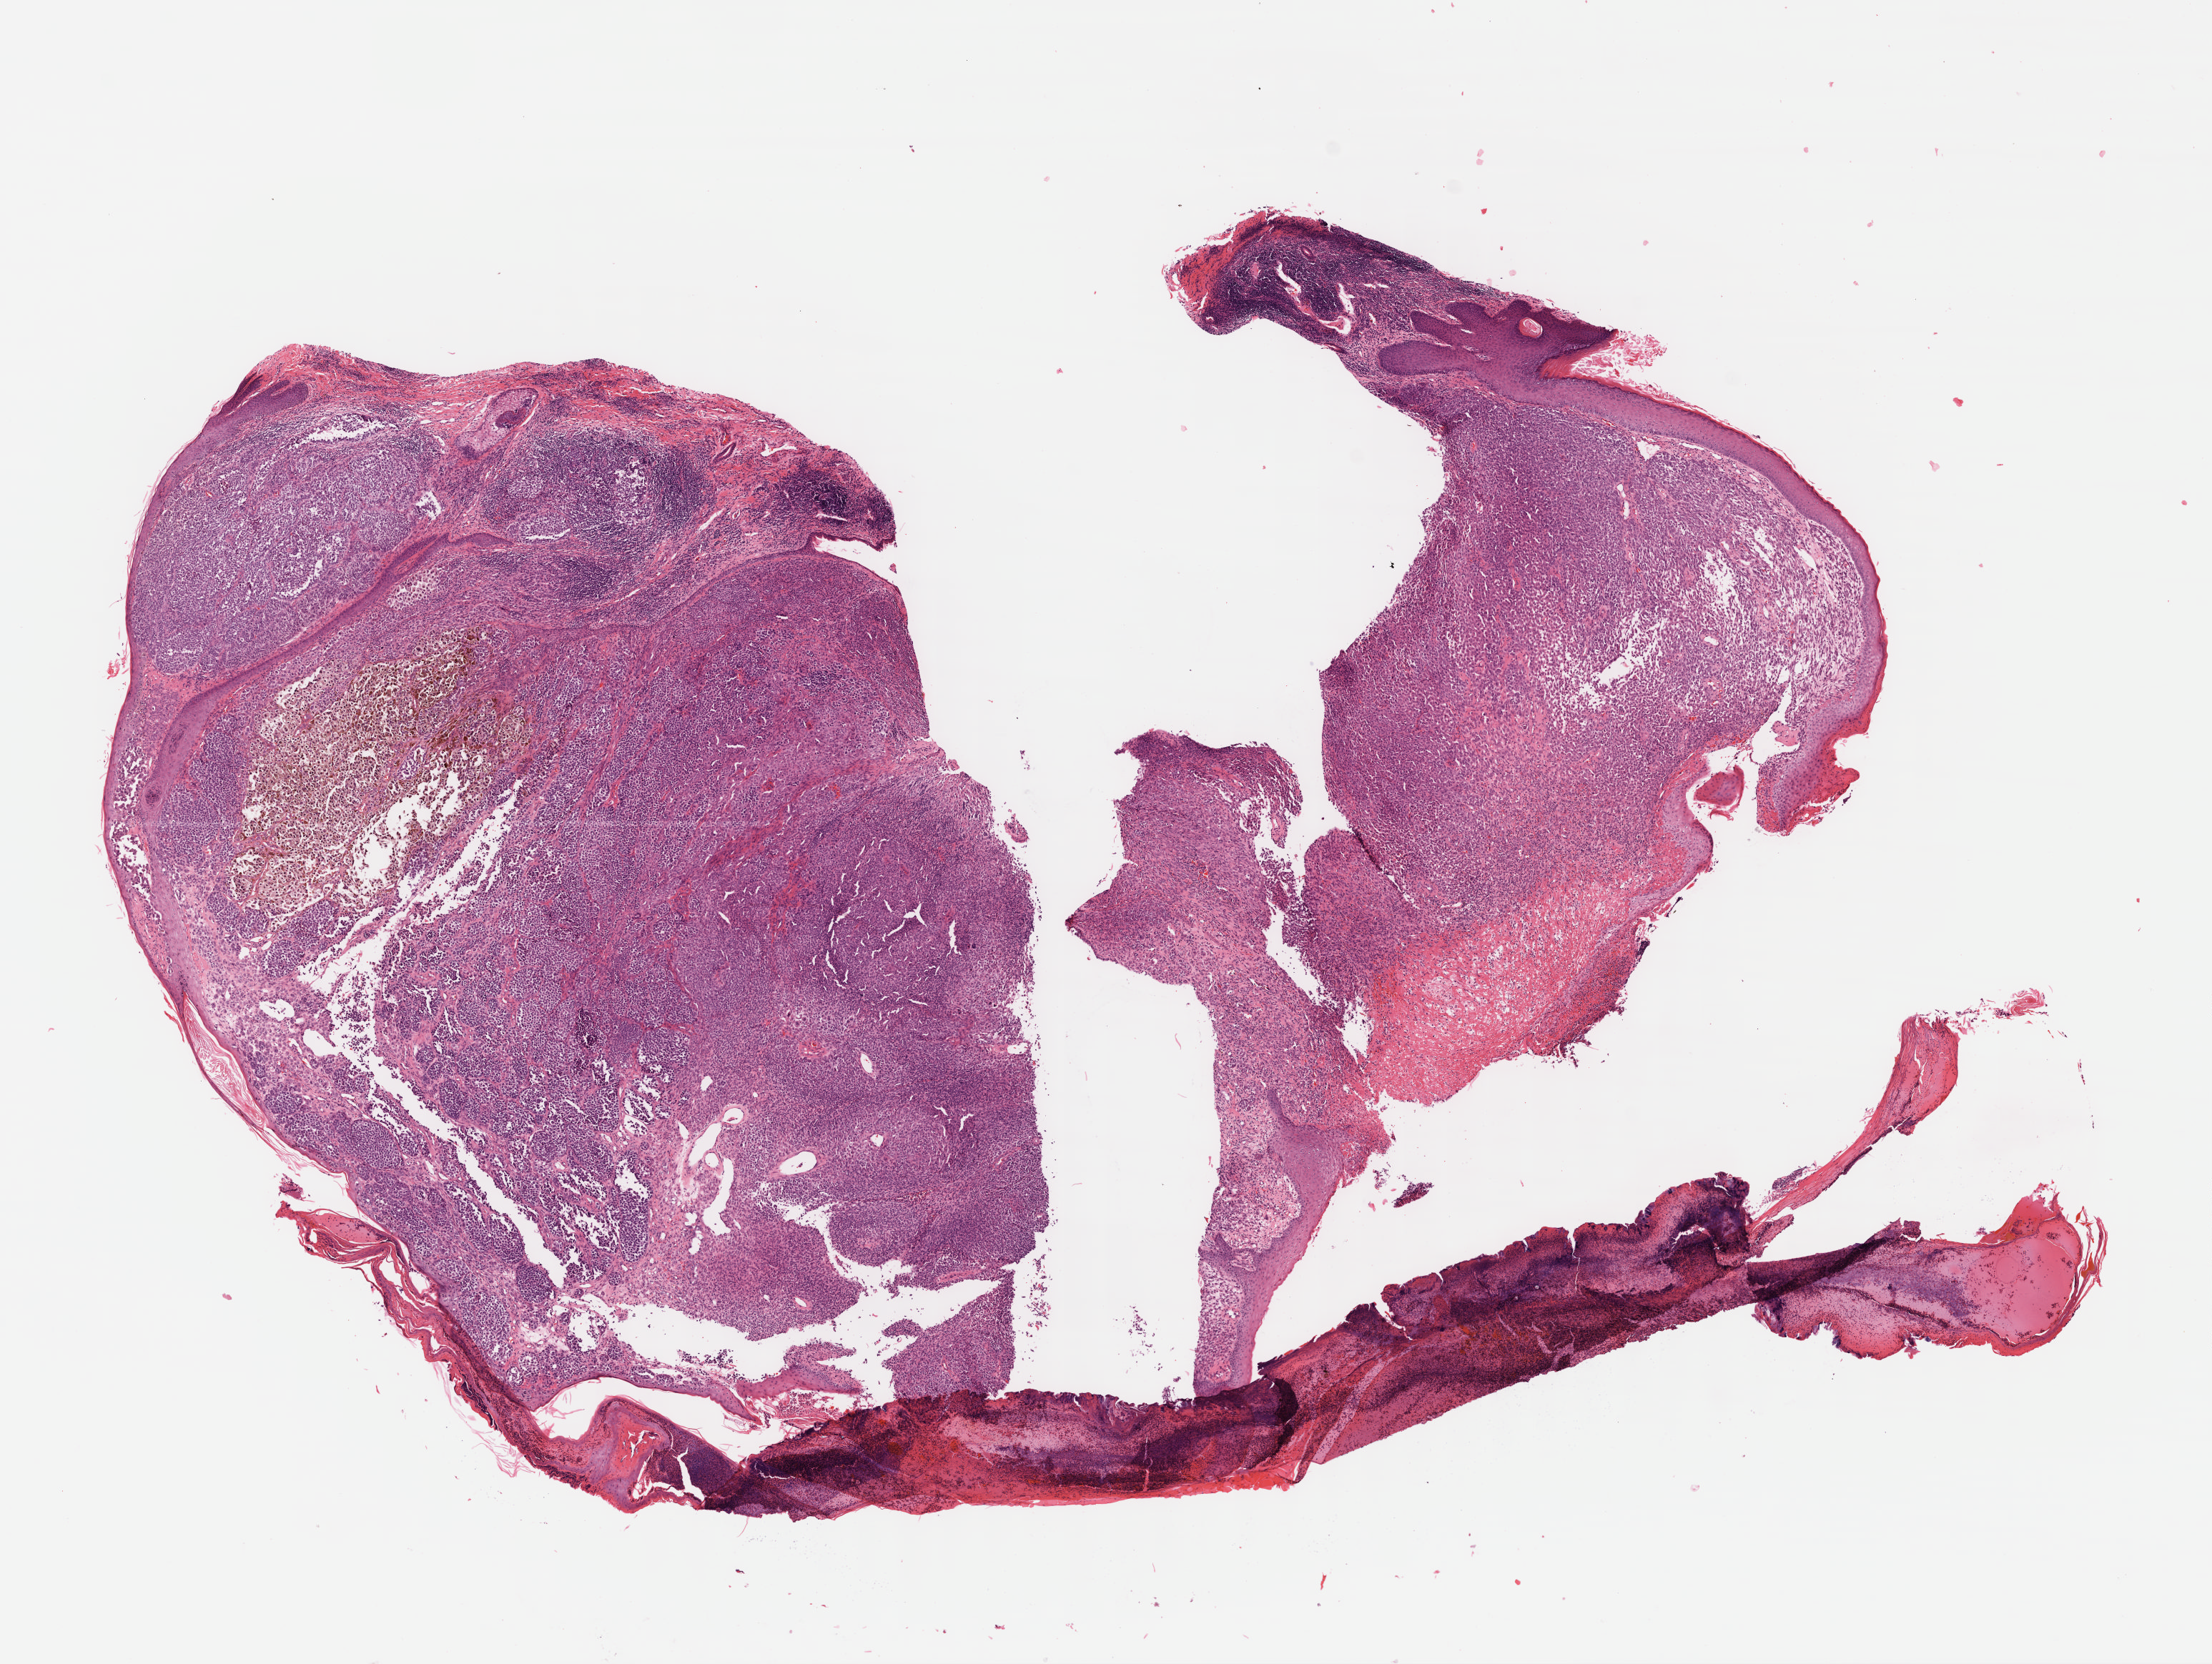
H&E-stained whole-slide image, shown as a low-resolution overview of the whole scanned area (about 12.2 x 9.1 mm, from a 40x scan); formalin-fixed paraffin-embedded (FFPE) diagnostic section; sample: primary tumour, skin. Male patient; age at initial diagnosis 59 years.
- AJCC pathologic stage: IIC (7th edition)
- pathologic diagnosis: Nodular melanoma